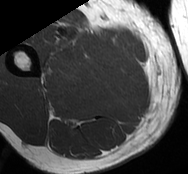
MRI of an extremity soft-tissue mass, one axial slice. Slice 22 of 93 in the series (ordered by position). MR volume resampled by the dataset authors to the PET/CT grid (not the native acquisition matrix). 3.27 mm slice thickness. 188 × 174 image matrix, field of view 184 × 170 mm. Male patient. Case-level facts recorded for this patient, not image findings: histological type: undifferentiated - pleiomorphic; grade: high; site of the primary tumour: right thigh.
Outlined on this slice (expert contour drawn on MRI and transferred to this co-registered scan by the dataset authors):
- gross tumour volume including surrounding oedema: bounding box <50,35,123,73> (left, top, right, bottom; pixels)